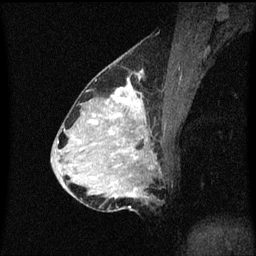
Breast MRI (dynamic contrast-enhanced), one sagittal slice. Slice 29 of 60 in the series (ordered by position). Dynamic contrast-enhanced series, image 2 of 3 at this slice position (ordered by acquisition). 1.5 T. TE 4.2 ms, TR 8.4 ms. 2 mm slice thickness. 256 × 256 image matrix, field of view 200 × 200 mm. Female patient, age 34 years. Case-level facts recorded for this patient, not image findings: setting: breast cancer imaged before/during neoadjuvant chemotherapy; receptor status: HR-positive, HER2-negative.
Structures marked on this image (semi-automatically segmented with operator editing):
- analysis volume of interest (the breast-tissue region the enhancement analysis was run in; not a lesion): bounding box (x1, y1, x2, y2) in pixels: (69, 70, 162, 209)
- tumour enhancement mask (voxels above the 70 % enhancement threshold inside the analysis volume of interest): (110, 84, 144, 159)